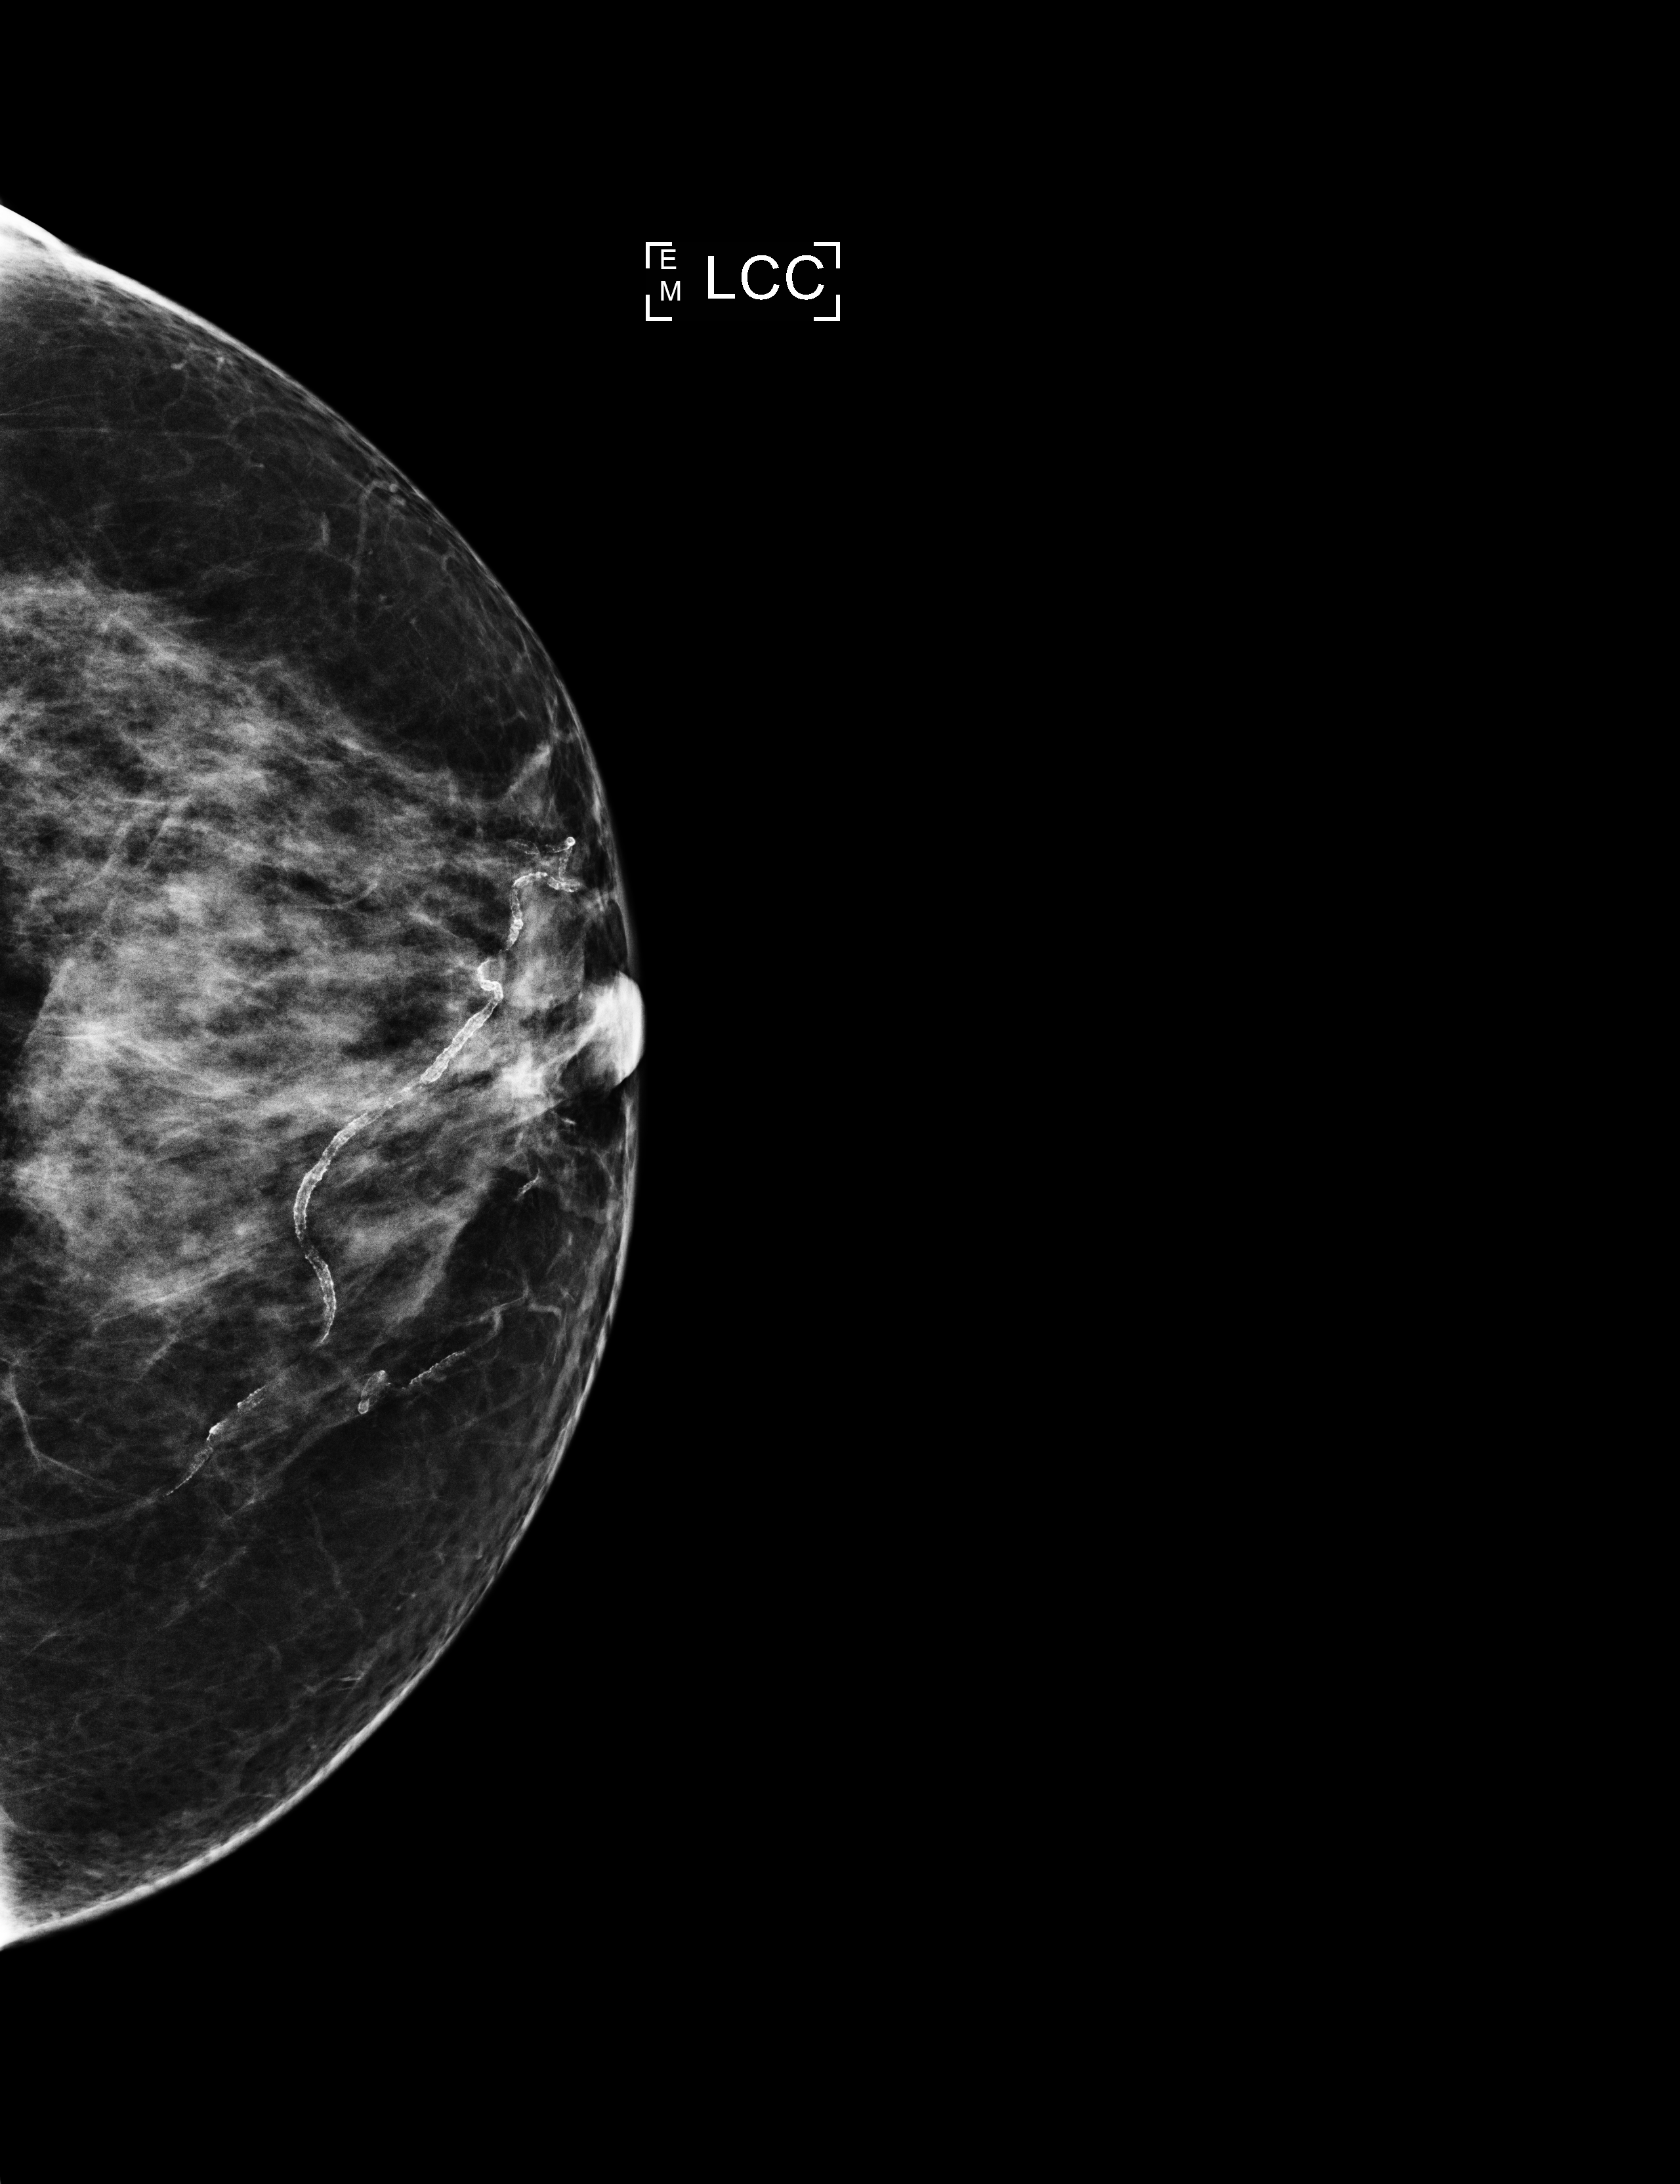
Full-field digital mammogram (FFDM); left breast; craniocaudal (CC) view; screening examination. Patient aged 59 years (female).
- breast density at the screening exam (both breasts): heterogeneously dense (BI-RADS density category c)
- final BI-RADS category for the screening round (tomosynthesis exam, both breasts): category 1
- recall: no recall after this screen